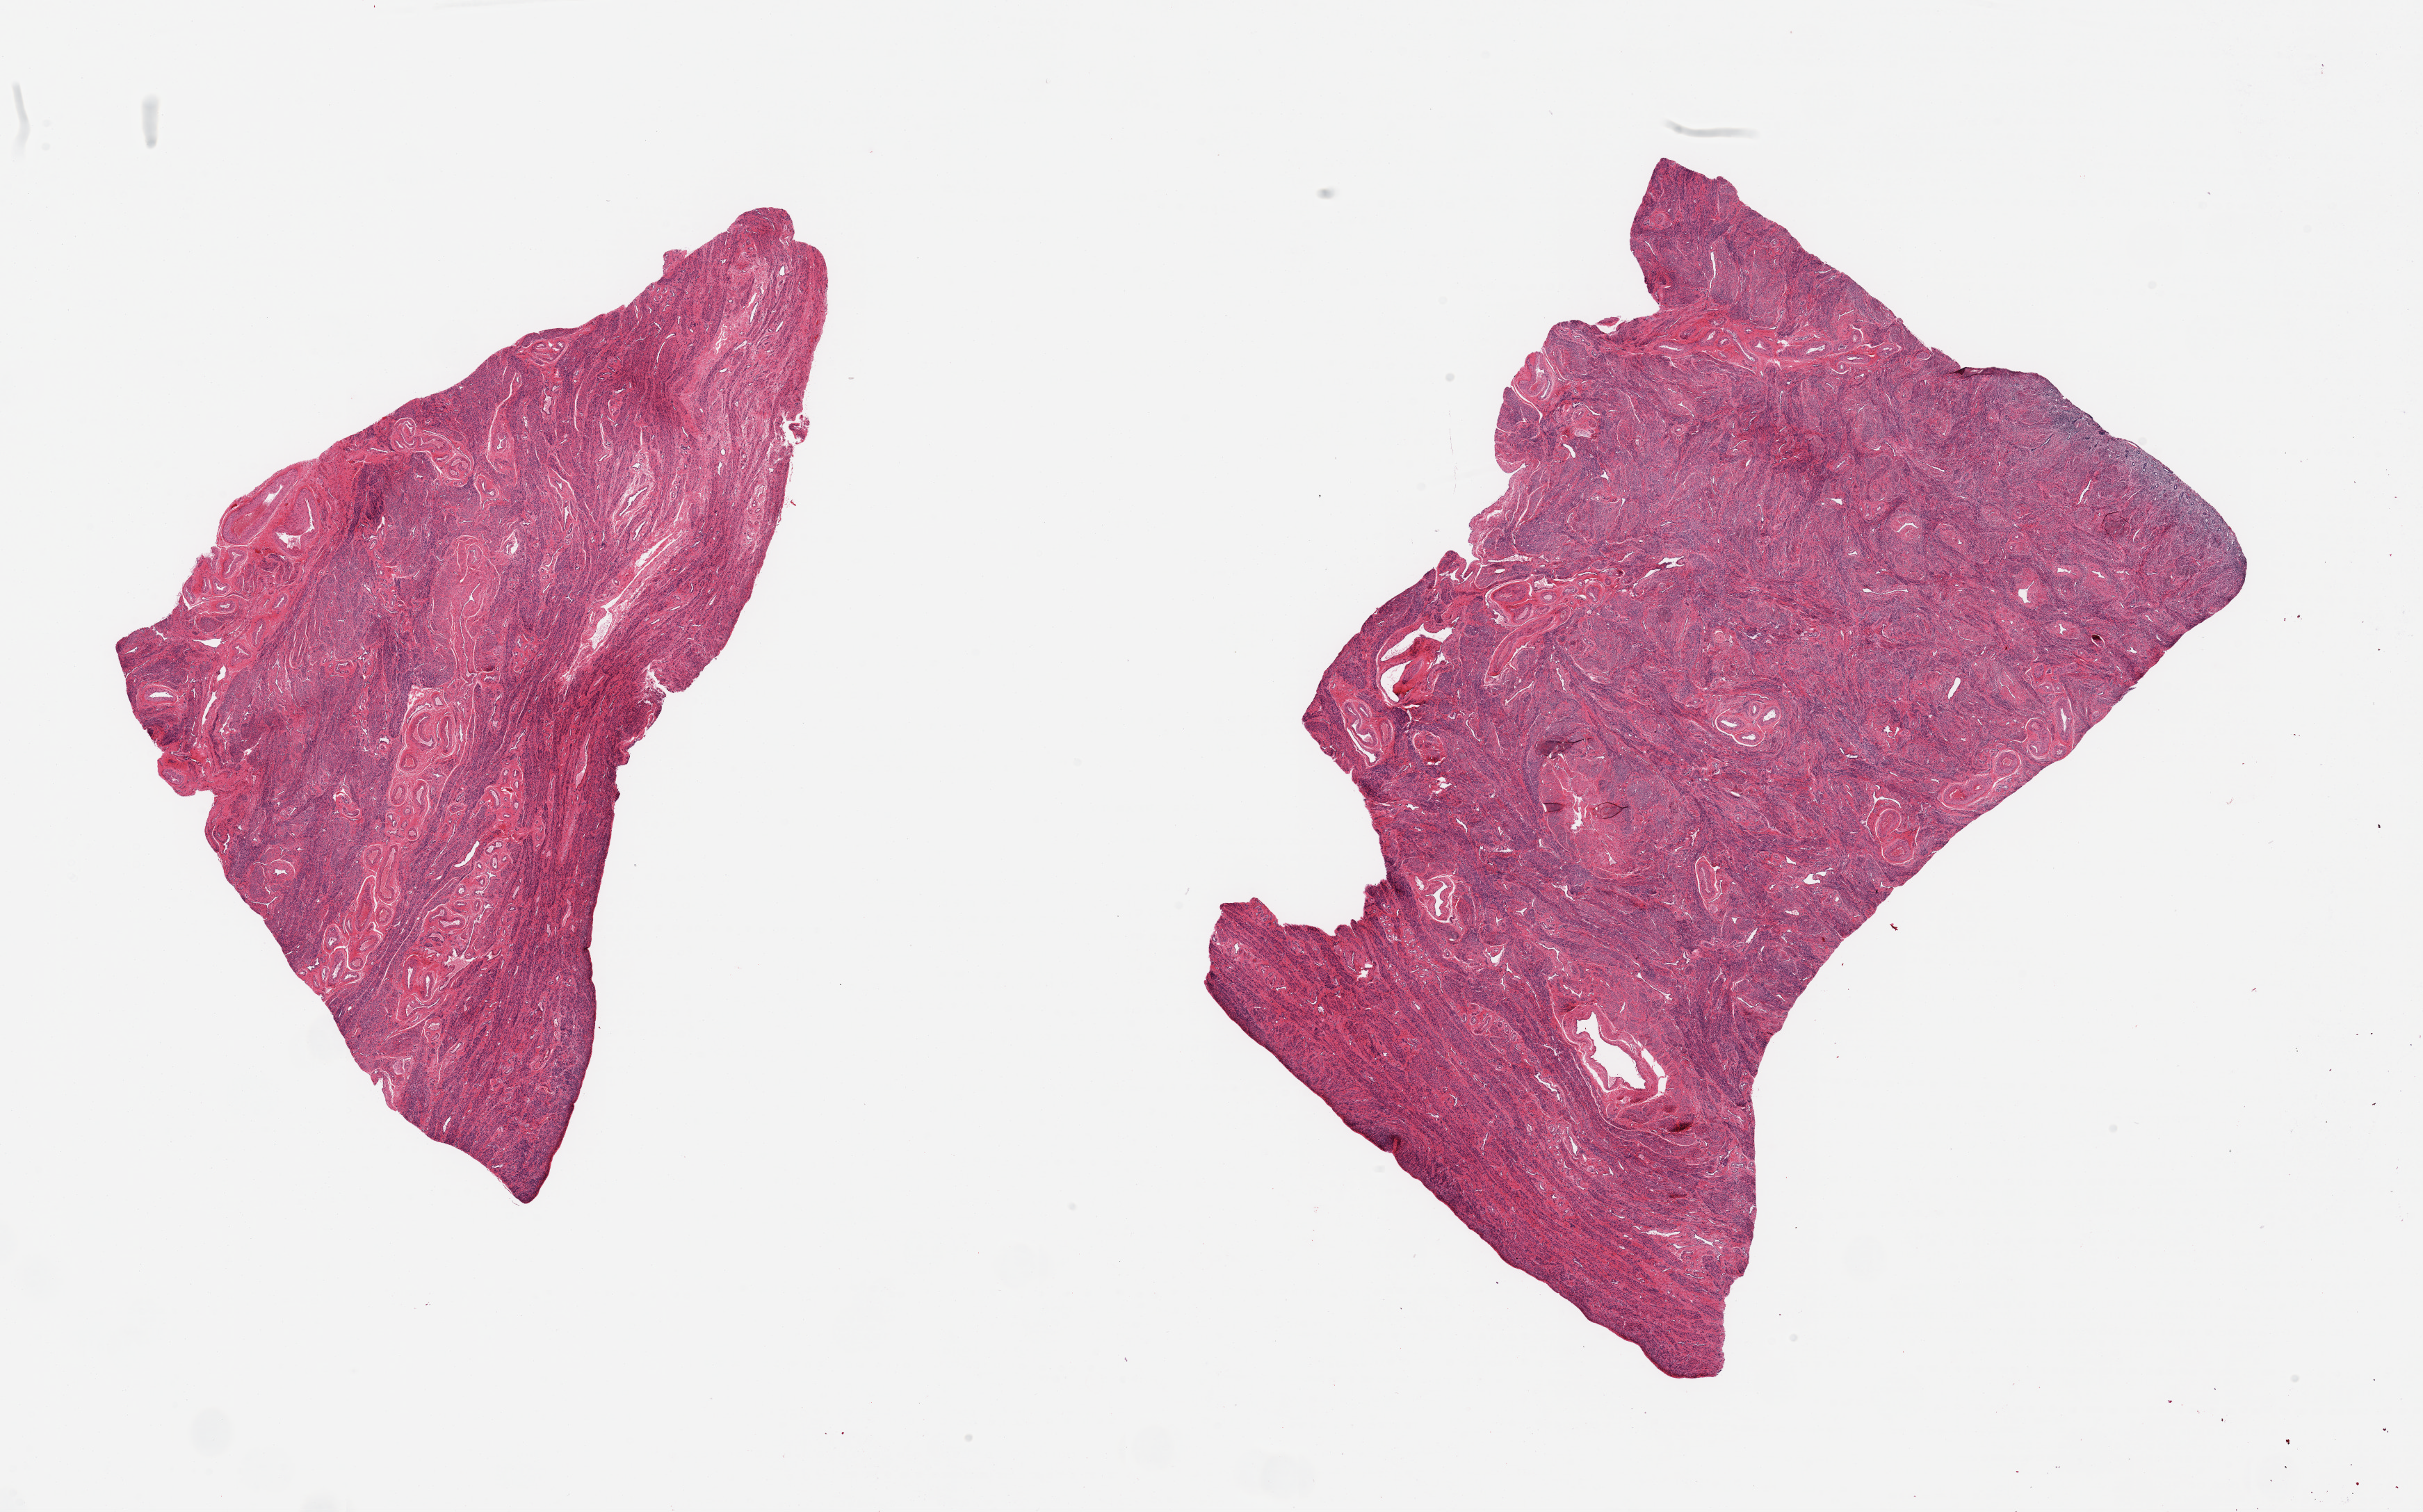
Digitized H&E-stained section, low-resolution overview of the scanned area, about 27.6 x 17.2 mm (from a 20x scan). PAXgene-fixed, paraffin-embedded tissue. Section of uterus (target tissue). Tissue donor sample. Female donor.
Reviewer comment on this tissue sample: 2 pieces, myometrium; trace residual basalis endometrium (~0.5mm).